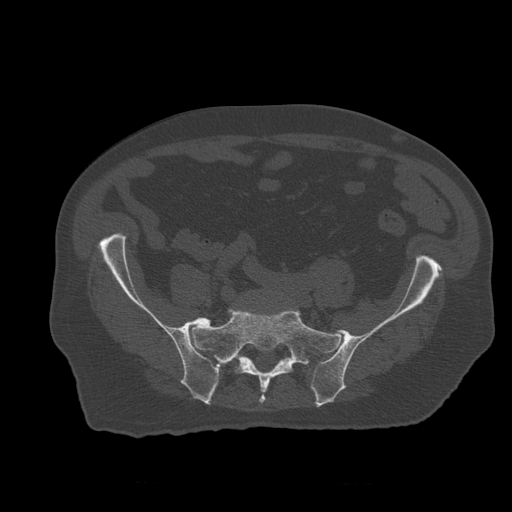
CT including the spine, one axial slice; slice 121 of 399 in the series (ordered by position); bone window (W 1800 / L 400 HU); 1.25 mm slice thickness; 512 × 512 image matrix, field of view 407 × 407 mm. Patient age 73 years. Case-level facts recorded for this patient, not image findings: primary cancer: prostate; vertebrae with lytic lesions (as recorded): L2.
Annotated regions visible in this slice (semi-automatic segmentation, software-assisted and operator-edited):
- L5 vertebra: box from (x=213, y=361) to (x=228, y=378) px